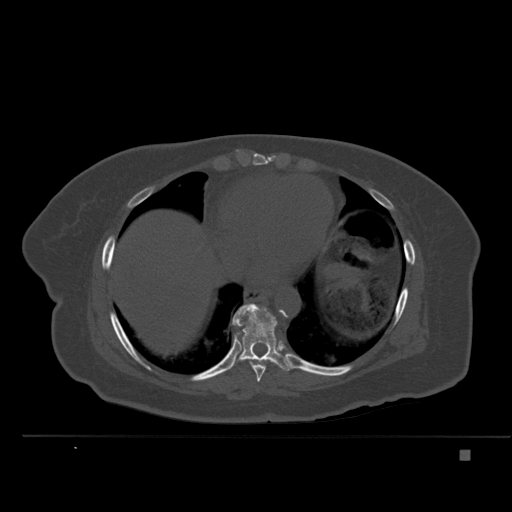
CT including the spine, one axial slice; position 302 of 477 along the scan axis; bone window (W 1800 / L 400 HU); 512 × 512 image matrix. Patient: female, 74 years. From the clinical record (not read from this slice): primary cancer: colon.
Outlined on this slice (semi-automatically segmented with operator editing):
- T8 vertebra: bounding box <249,359,266,382> (left, top, right, bottom; pixels)
- T9 vertebra: <230,303,293,371>